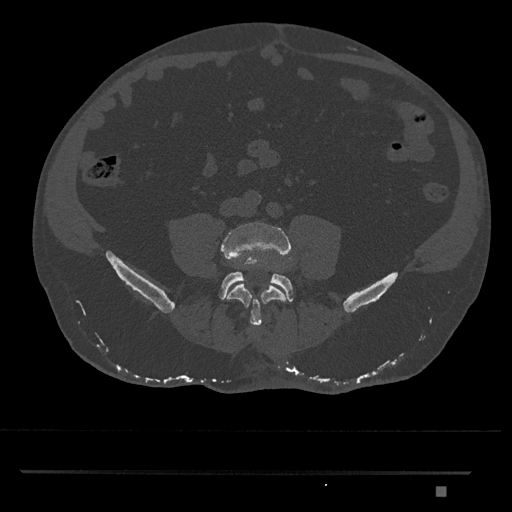
CT including the spine, one axial slice; position 587 of 1134 along the scan axis; reconstruction kernel Br40s/3; bone window (W 1800 / L 400 HU); 512 × 512 image matrix, field of view 429 × 429 mm. Patient: male, 65 years. Case-level facts recorded for this patient, not image findings: primary cancer: prostate.
Outlined on this slice (semi-automatic segmentation, software-assisted and operator-edited):
- L4 vertebra: bounding box [x1, y1, x2, y2] px = [220, 222, 294, 328]
- L5 vertebra: [218, 272, 294, 302]